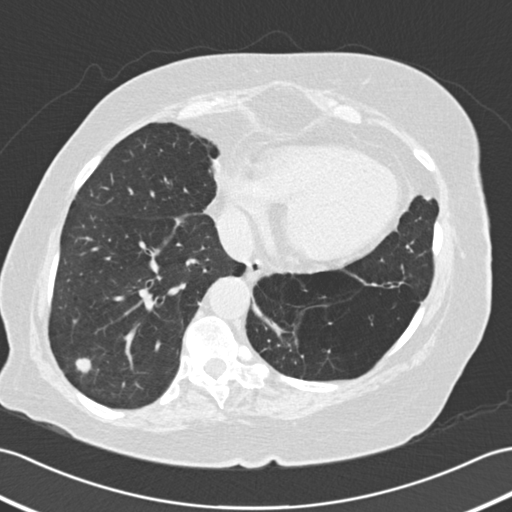
Low-dose screening chest CT, one axial slice. Slice 58 of 161 in the series (ordered by position). Lung window (W 1500 / L -600 HU). 512 × 512 image matrix, field of view 353 × 353 mm.
Annotated regions visible in this slice (expert manual segmentation):
- lesion 1 (tumor, lower lobe of right lung): bounding box [x1, y1, x2, y2] px = [76, 358, 91, 373]